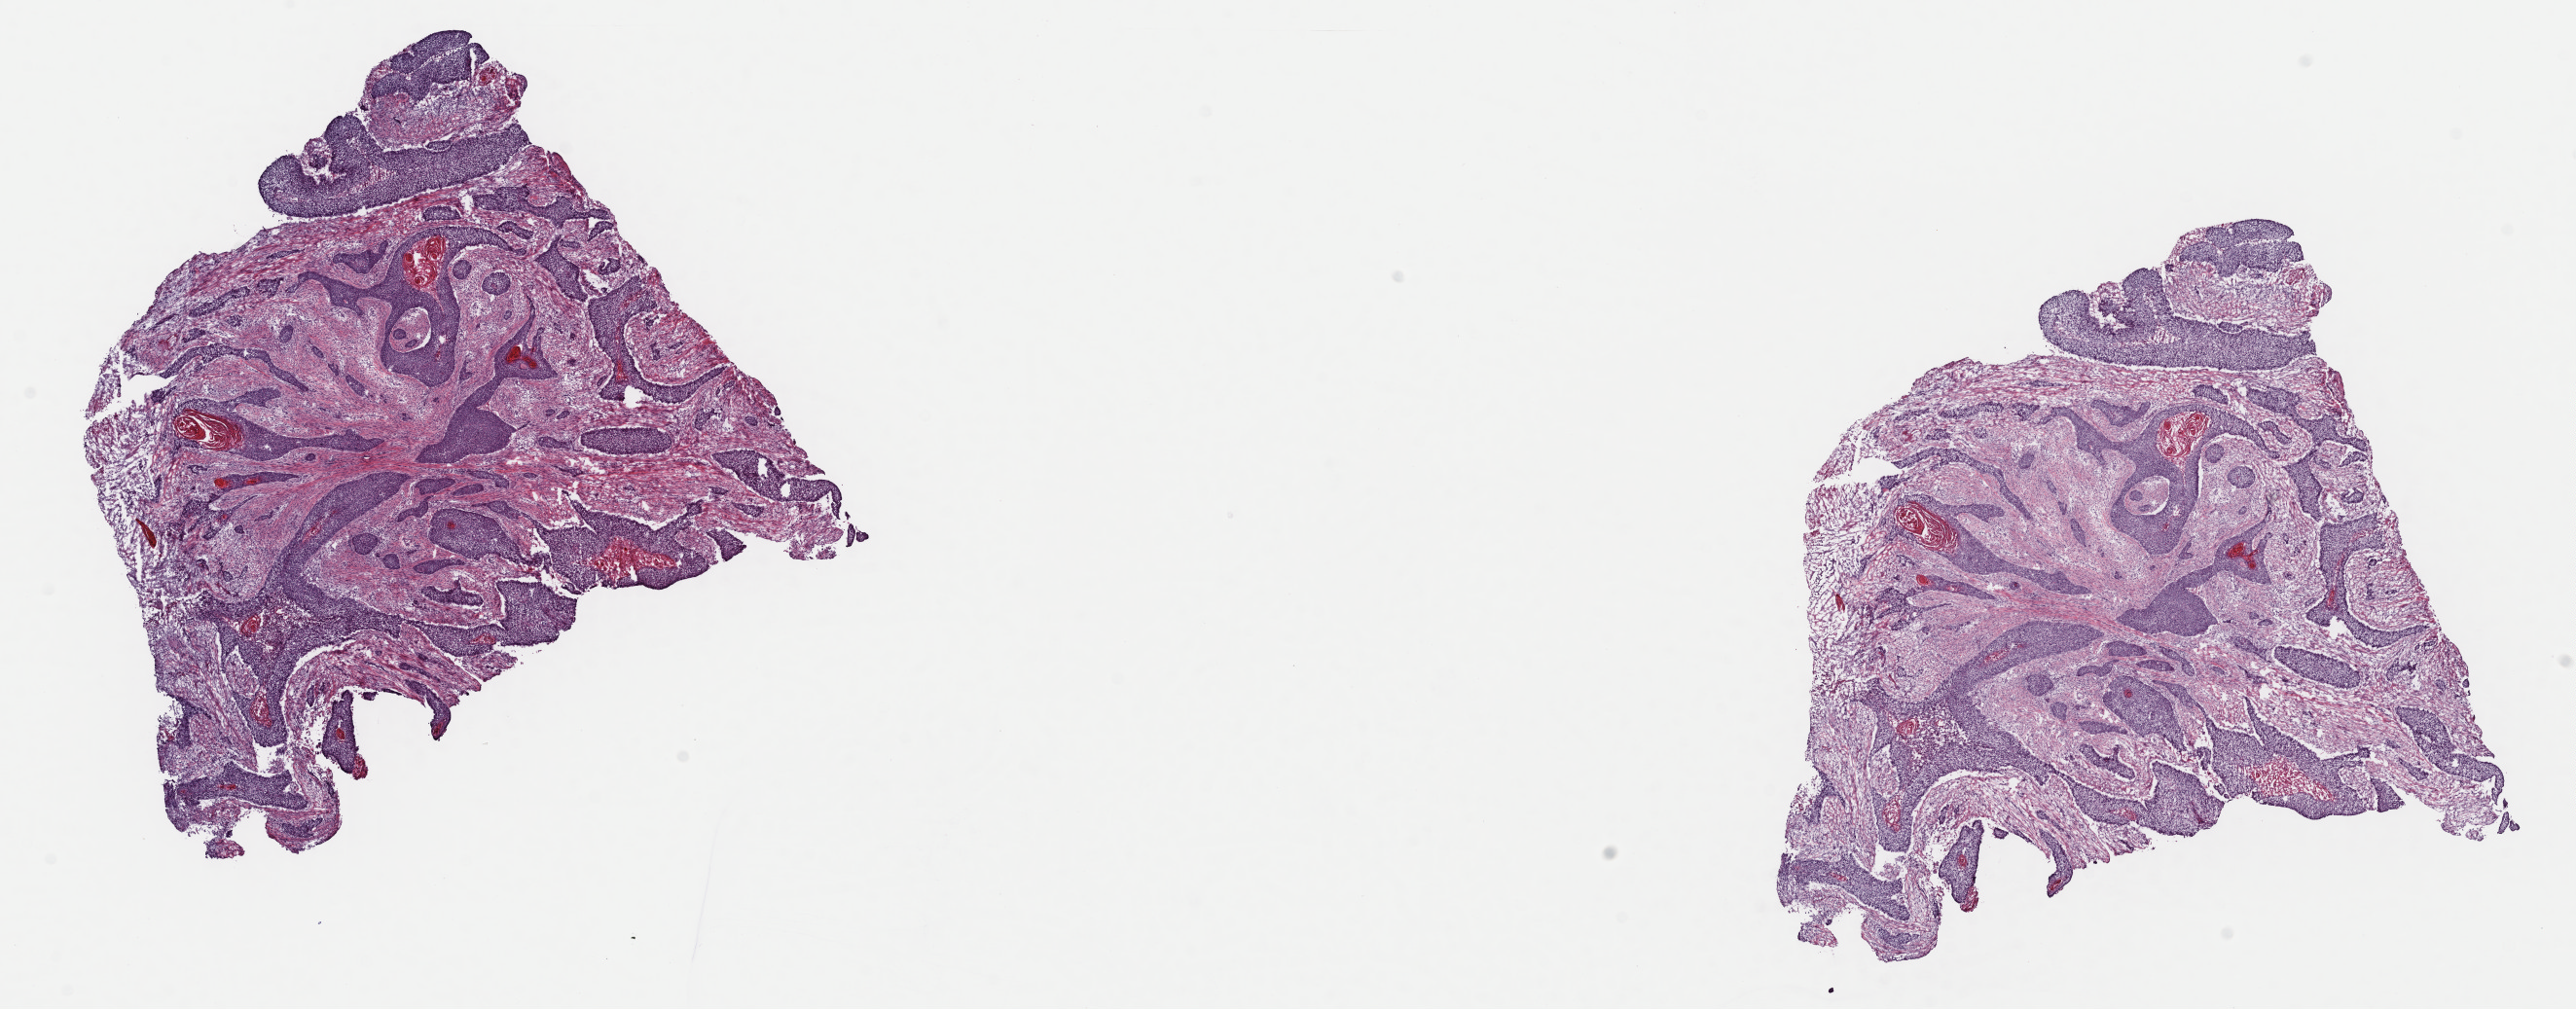
Digitized Hematoxylin and eosin (H&E) stained tissue section (whole slide) — a low-resolution overview of the entire scanned area, about 20.9 x 8.2 mm (from a 40x scan); frozen section from the top of the tissue portion; primary tumour sample from the esophagus. Patient: male, age at initial diagnosis 51 years. Histologic grade: G1 (well differentiated). Composition of this section per pathologist review: tumour cells 40%, tumour nuclei 75%, normal cells 0%, stromal cells 54%, necrosis 6%. Infiltration values recorded for this section: lymphocyte infiltration 4%, monocyte infiltration 1%, neutrophil infiltration 1%.
Diagnosis: Squamous cell carcinoma, NOS. AJCC pathologic stage: IB (7th edition).